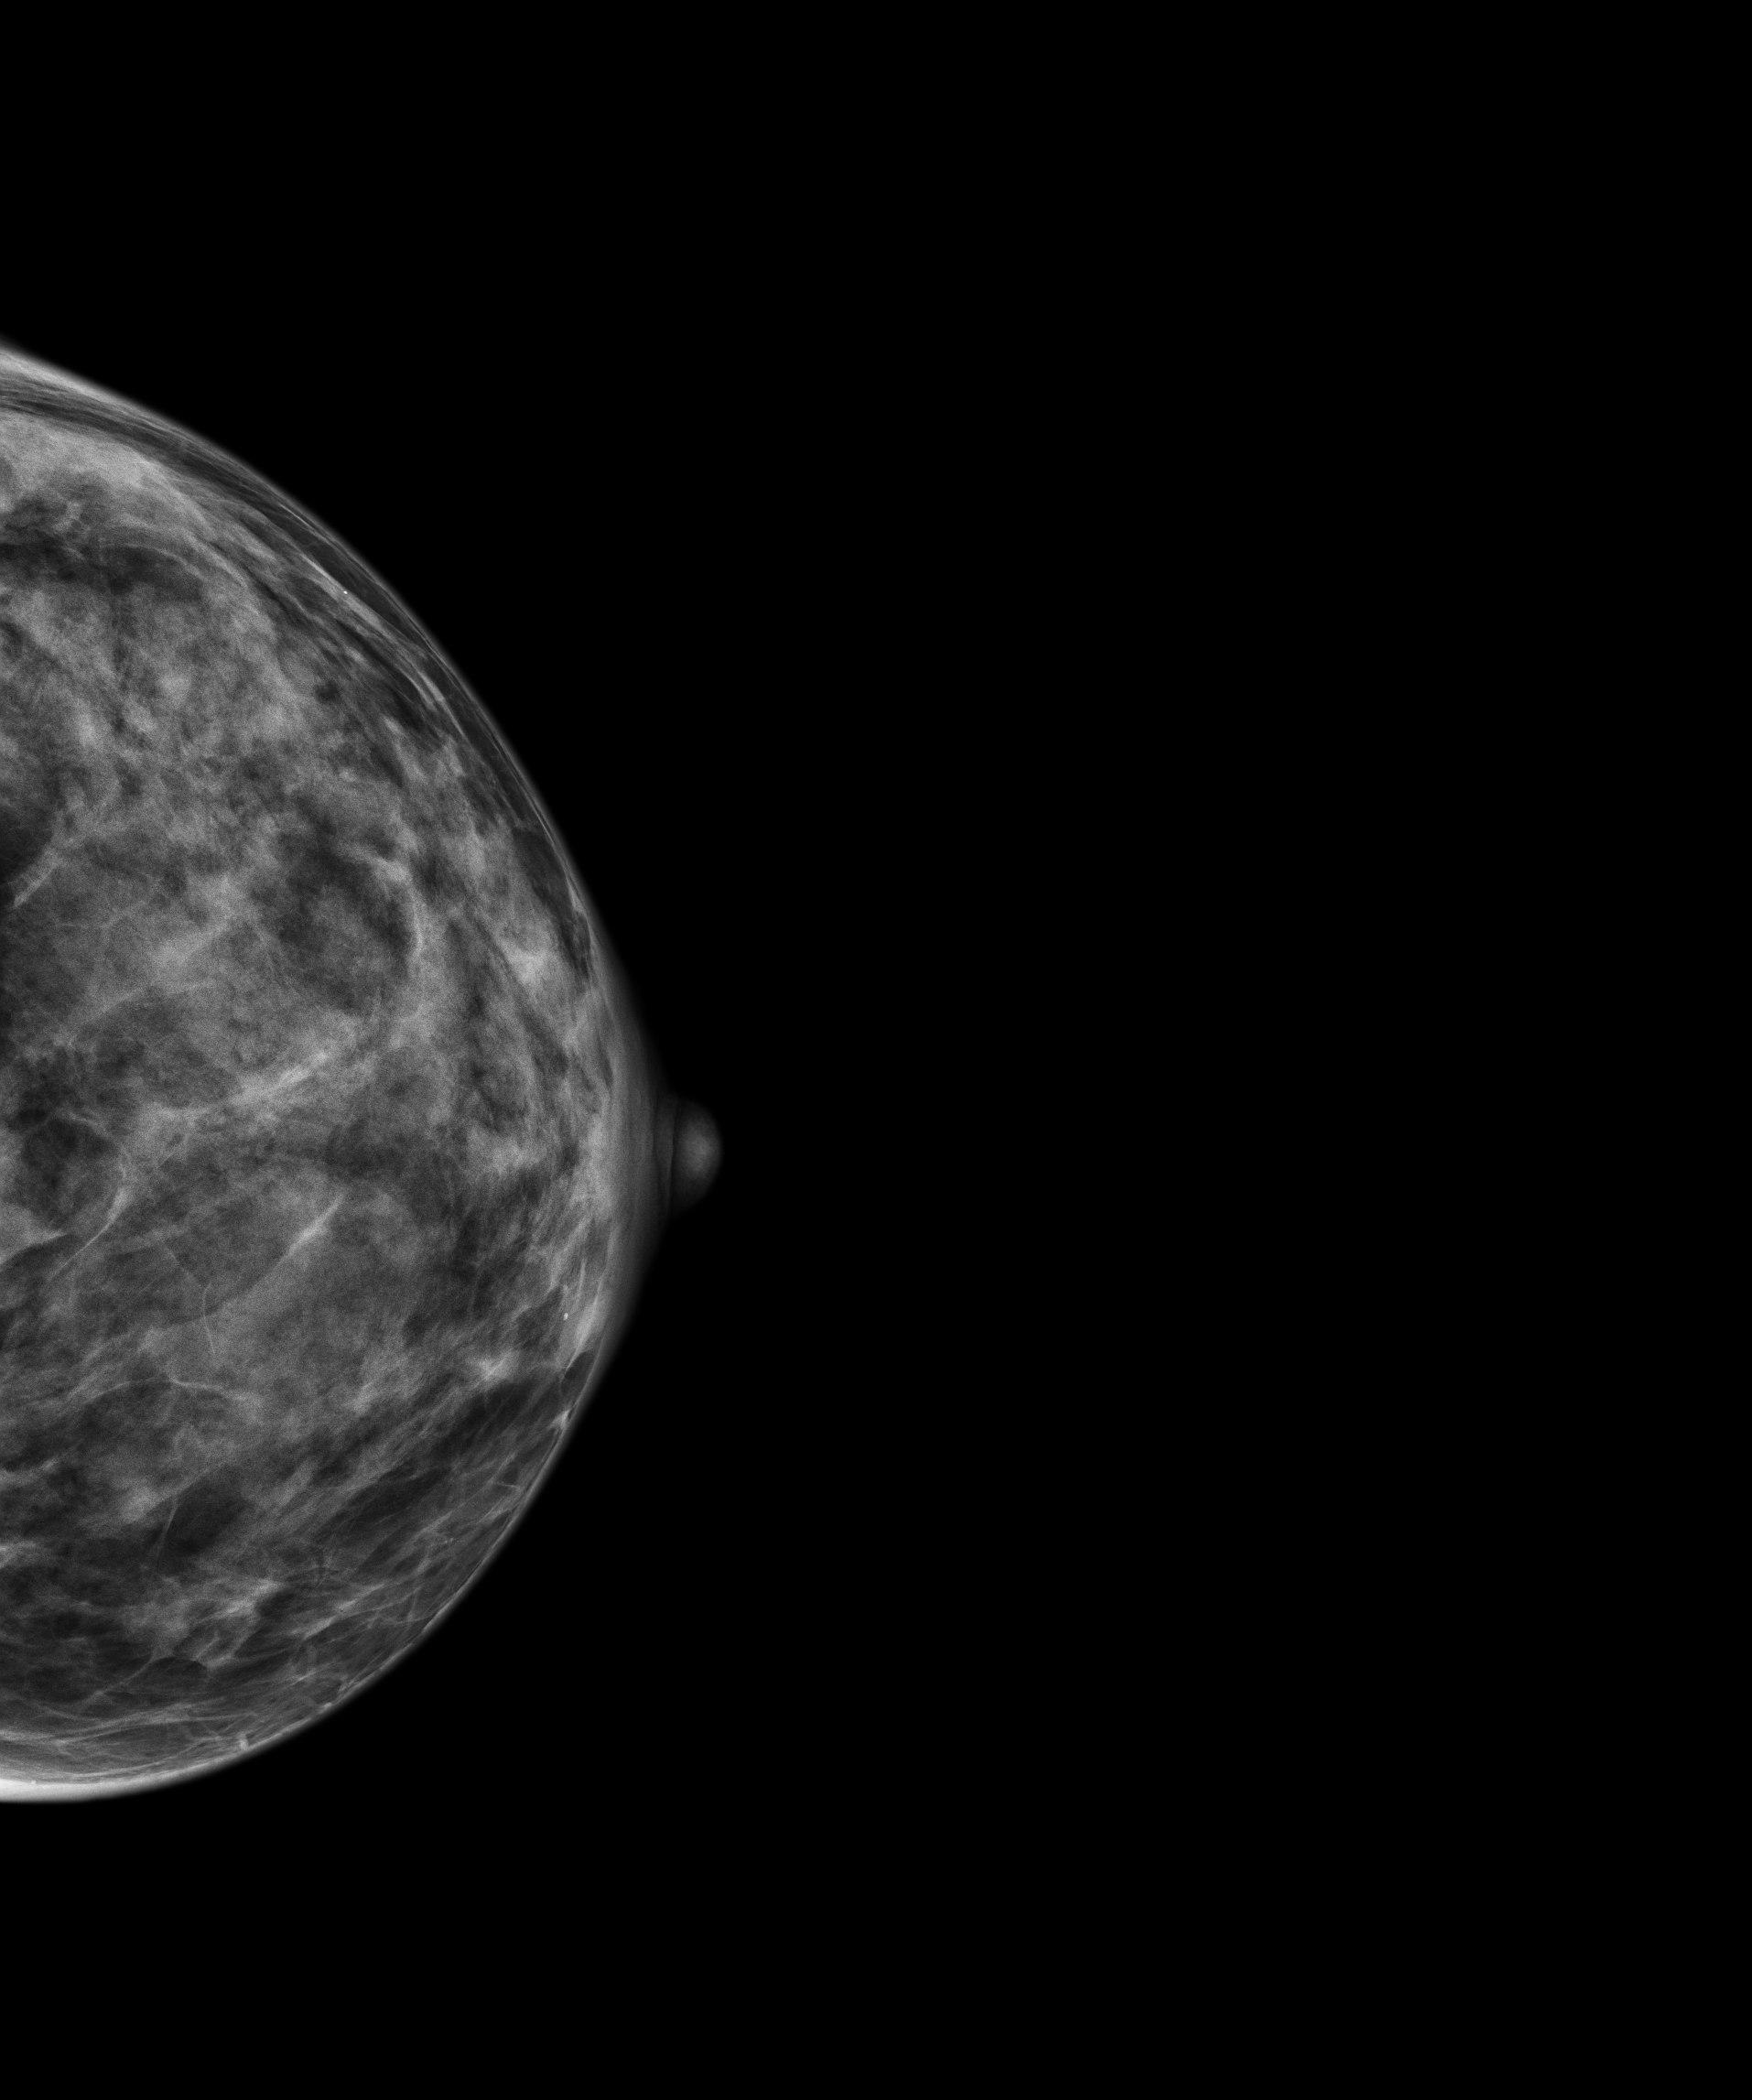
Digital mammogram (FFDM); left breast; CC view; annual screening mammography examination; compressed breast thickness 35 mm; system: Senographe Essential ADS_56.21.3. Patient aged 45 years (female).
- breast density at the screening exam (both breasts): heterogeneously dense (BI-RADS density category c)
- final BI-RADS category for the screening round (tomosynthesis exam, both breasts): category 1
- recall: no recall after this screen